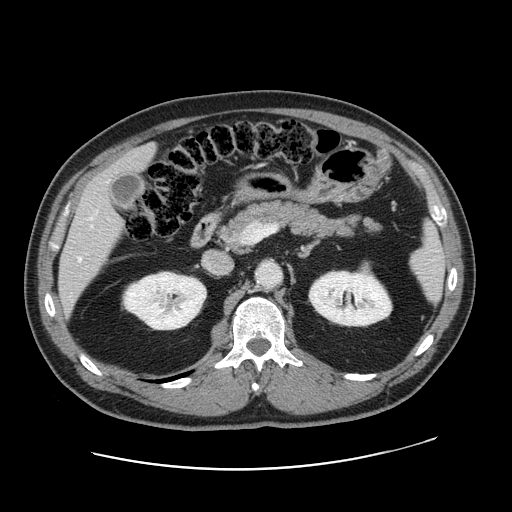
Contrast-enhanced abdominal CT, one axial slice. 120 kVp. Intravenous contrast given. Soft-tissue window (W 400 / L 40 HU). 2.5 mm slice thickness. 512 × 512 image matrix, field of view 403 × 403 mm. Male patient, age 63 years. Case-level facts recorded for this patient, not image findings: diagnosis: colorectal cancer liver metastases, imaged before liver resection; multiple liver metastases: yes; largest metastasis: 8 cm; disease in both lobes: yes.
Structures marked on this image (expert manual segmentation):
- hepatic veins: bounding box <79,218,92,261> (left, top, right, bottom; pixels)
- liver: <60,146,154,307>
- planned liver remnant (the part of the liver to remain after resection): <112,146,155,173>